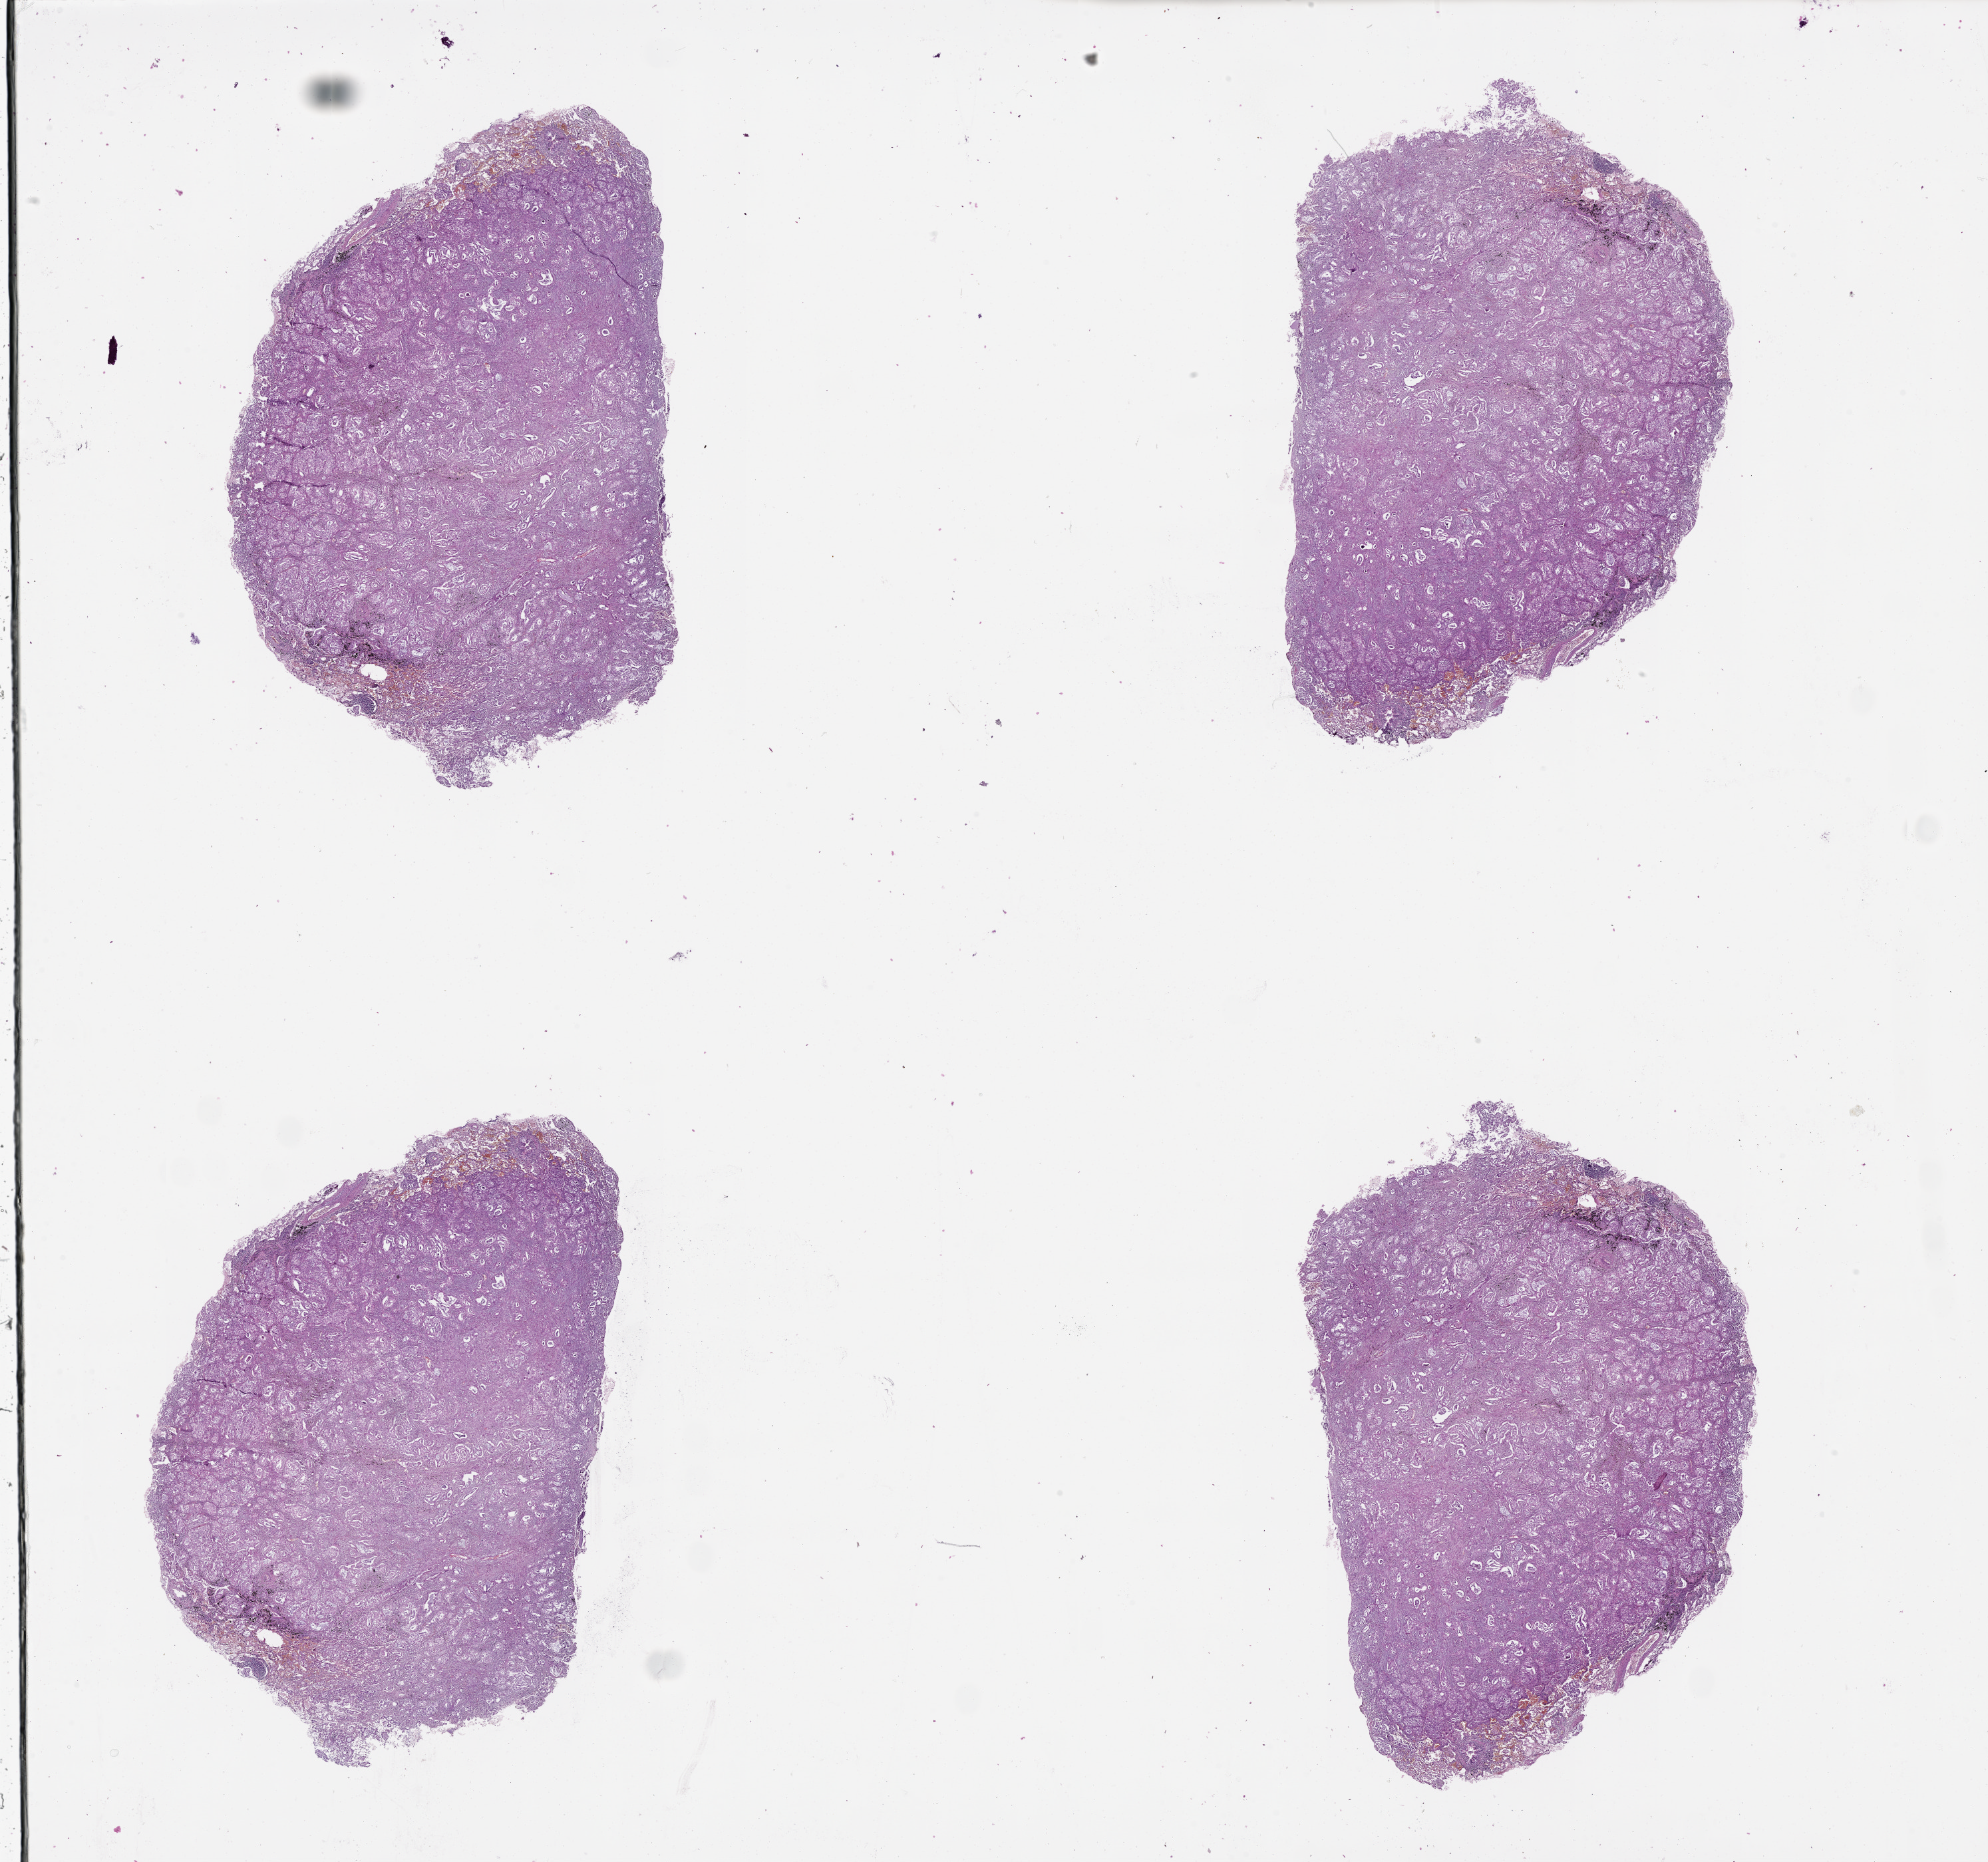
Whole-slide histology image, H&E — shown as a low-resolution overview of the whole scanned area (about 24.1 x 22.5 mm); lung, tissue type not recorded.
Patient diagnosis (cohort enrolment): lung adenocarcinoma (lung).